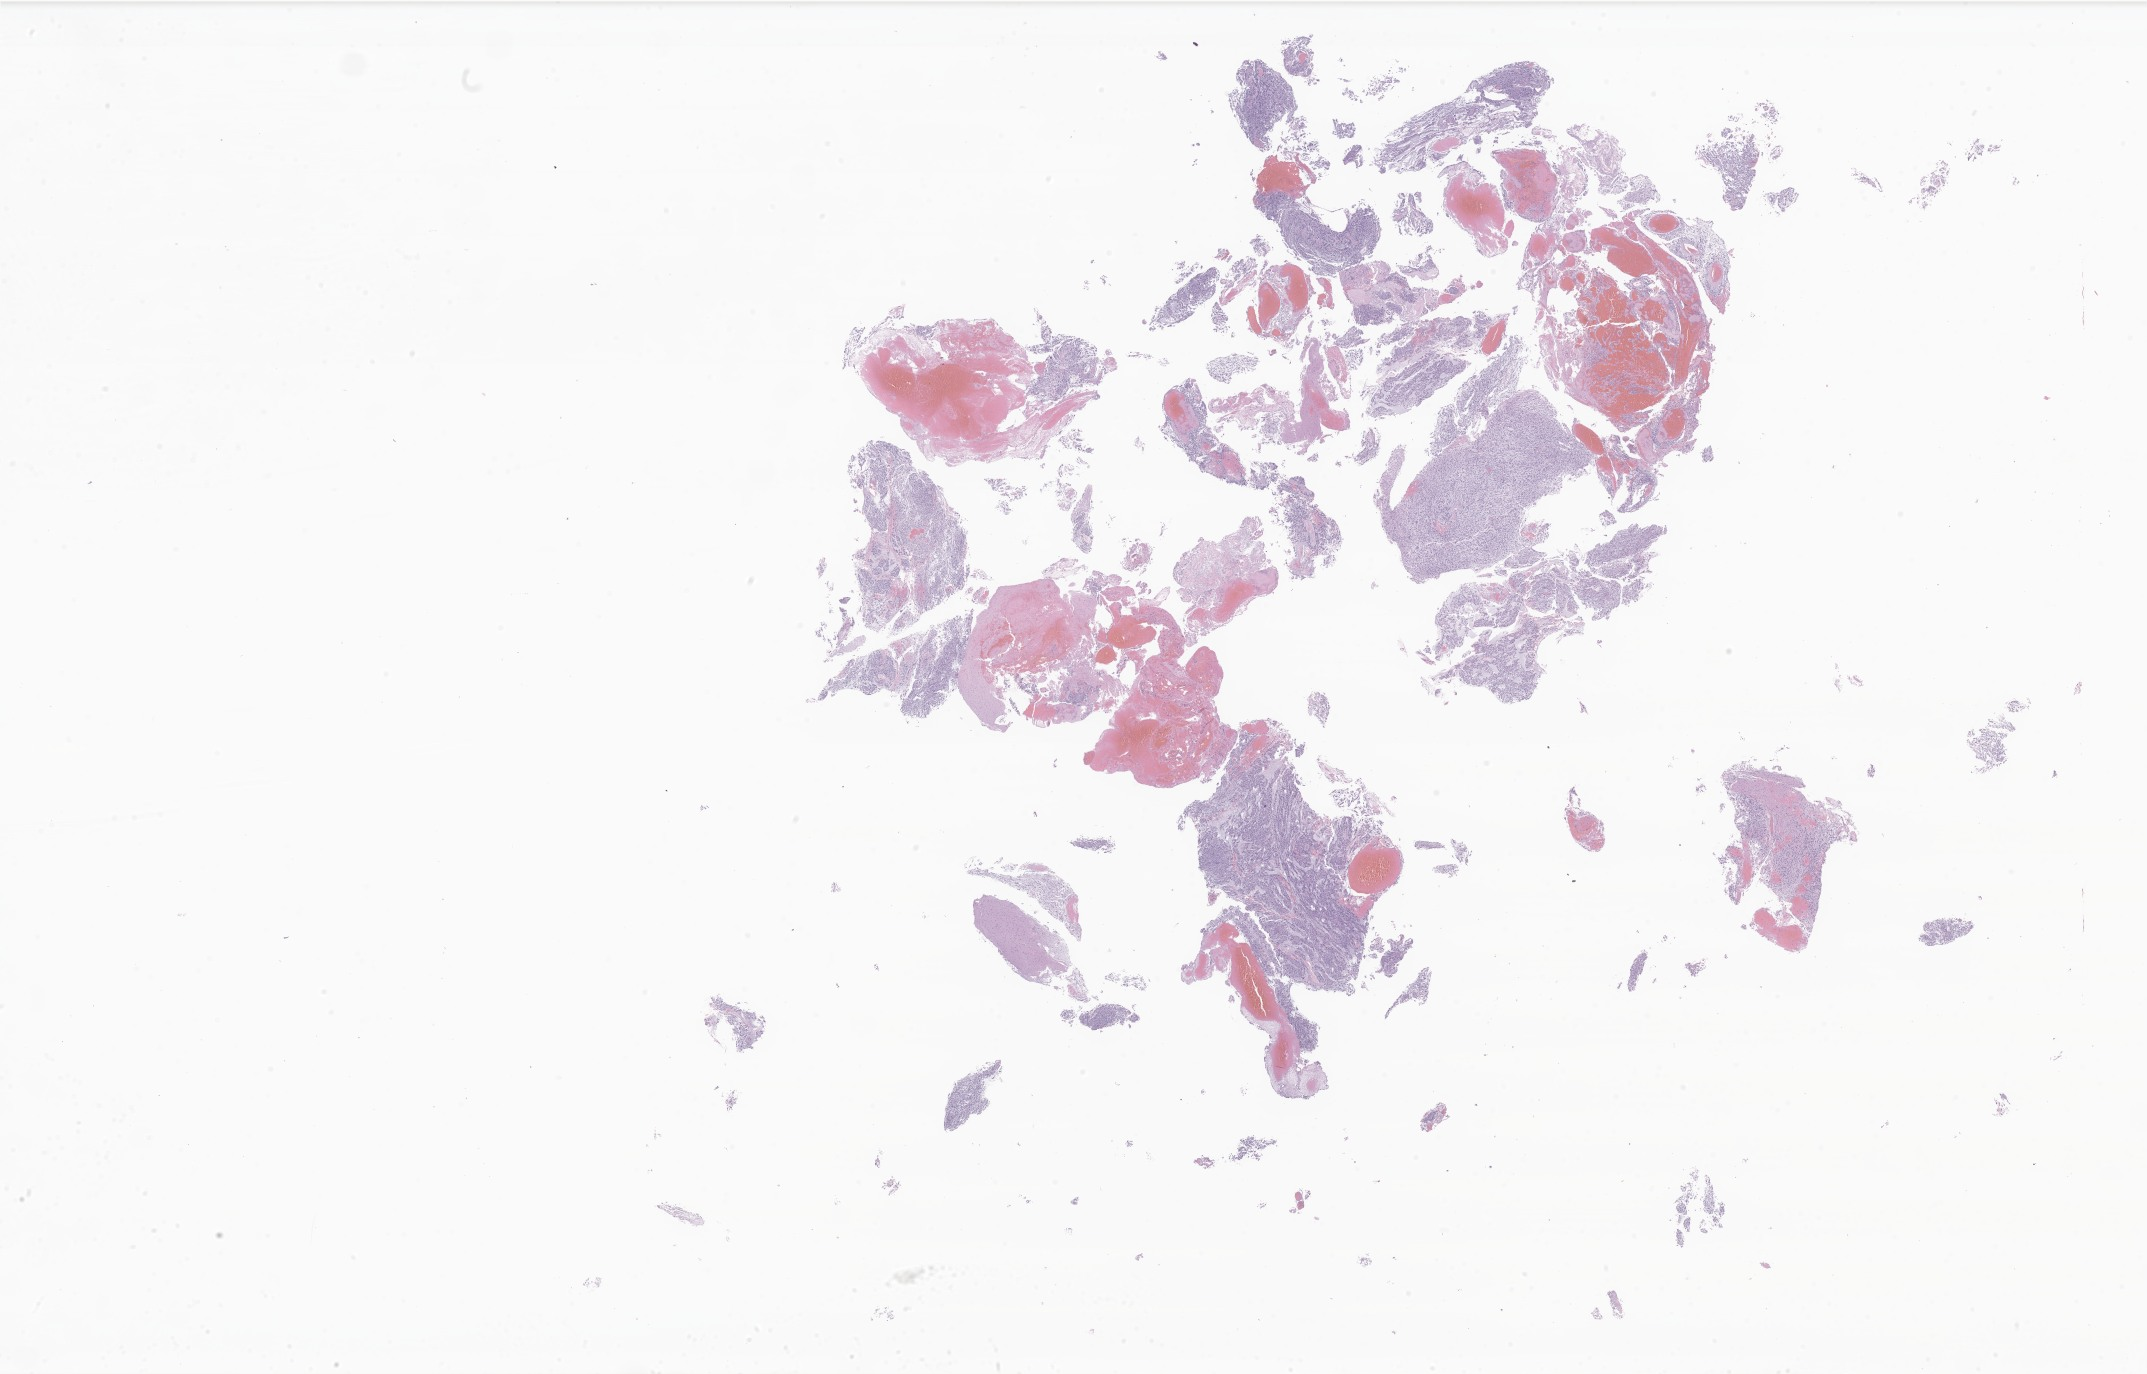
Digitized hematoxylin and eosin (H&E)-stained section of tumor tissue from the brain, a low-resolution overview of the entire scanned area, about 36.2 x 23.2 mm. FFPE section. Patient: female, age 117 months (9 years 9 months).
- diagnosis: Glioma, malignant